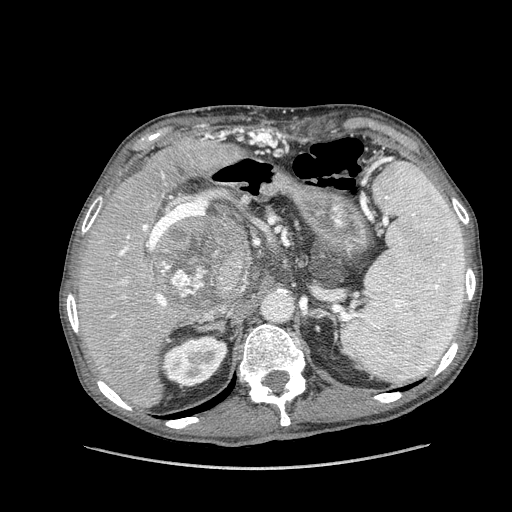
Contrast-enhanced abdominal CT (liver protocol), one axial slice; position 89 of 162 along the scan axis; reconstruction kernel STANDARD; 100 kVp; soft-tissue window (W 400 / L 40 HU); 2.5 mm slice thickness; 512 × 512 image matrix, field of view 400 × 400 mm. From the clinical record (not read from this slice): diagnosis: hepatocellular carcinoma (patient treated with transarterial chemoembolisation; whether this scan precedes or follows treatment is not stated here); TNM stage (as recorded): Stage-IIIA; Child-Pugh class: A; tumour nodularity: multinodular.
Outlined on this slice (semi-automatically segmented with operator editing):
- liver parenchyma outside the tumour (the mass and vessels are separate outlines, so this box may not span the whole liver): bounding box <78,133,250,408> (left, top, right, bottom; pixels)
- mass: <151,211,250,312>
- liver vessels: <109,134,213,368>